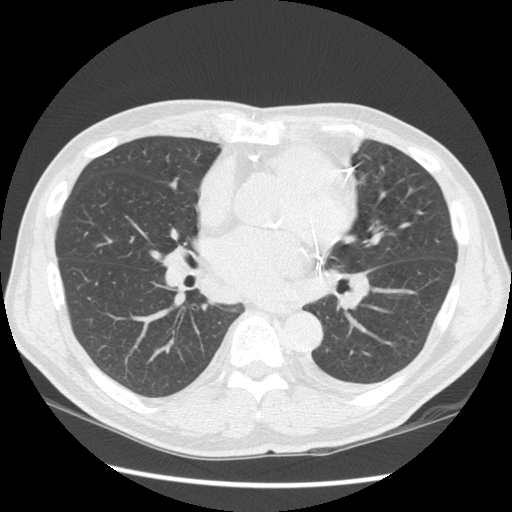
Low-dose screening chest CT, one axial slice. Slice 70 of 136 in the series (ordered by position). Reconstruction kernel STANDARD. Lung window (W 1500 / L -600 HU). 2.5 mm slice thickness. 512 × 512 image matrix, field of view 360 × 360 mm.
Annotated regions visible in this slice (manually delineated by an expert):
- lesion 1 (tumor, upper lobe of left lung): bounding box (x1, y1, x2, y2) in pixels: (335, 136, 360, 161)